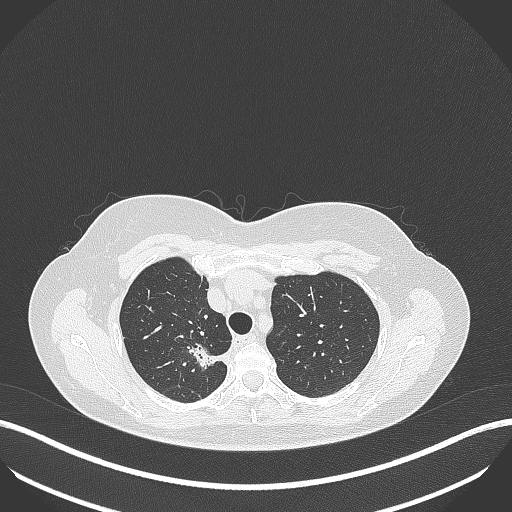
Chest CT, one axial slice. Slice 307 of 386 in the series (ordered by position). Reconstruction kernel B70f. 120 kVp. Lung window (W 1500 / L -600 HU). 512 × 512 image matrix. Patient: female, 65 years. Case-level facts recorded for this patient, not image findings: clinical TNM (as recorded): T1b N0 M0.
Annotated regions visible in this slice (bounding box drawn by a radiologist):
- lung tumour (recorded histology: adenocarcinoma): bounding box (x1, y1, x2, y2) in pixels: (184, 339, 233, 376)